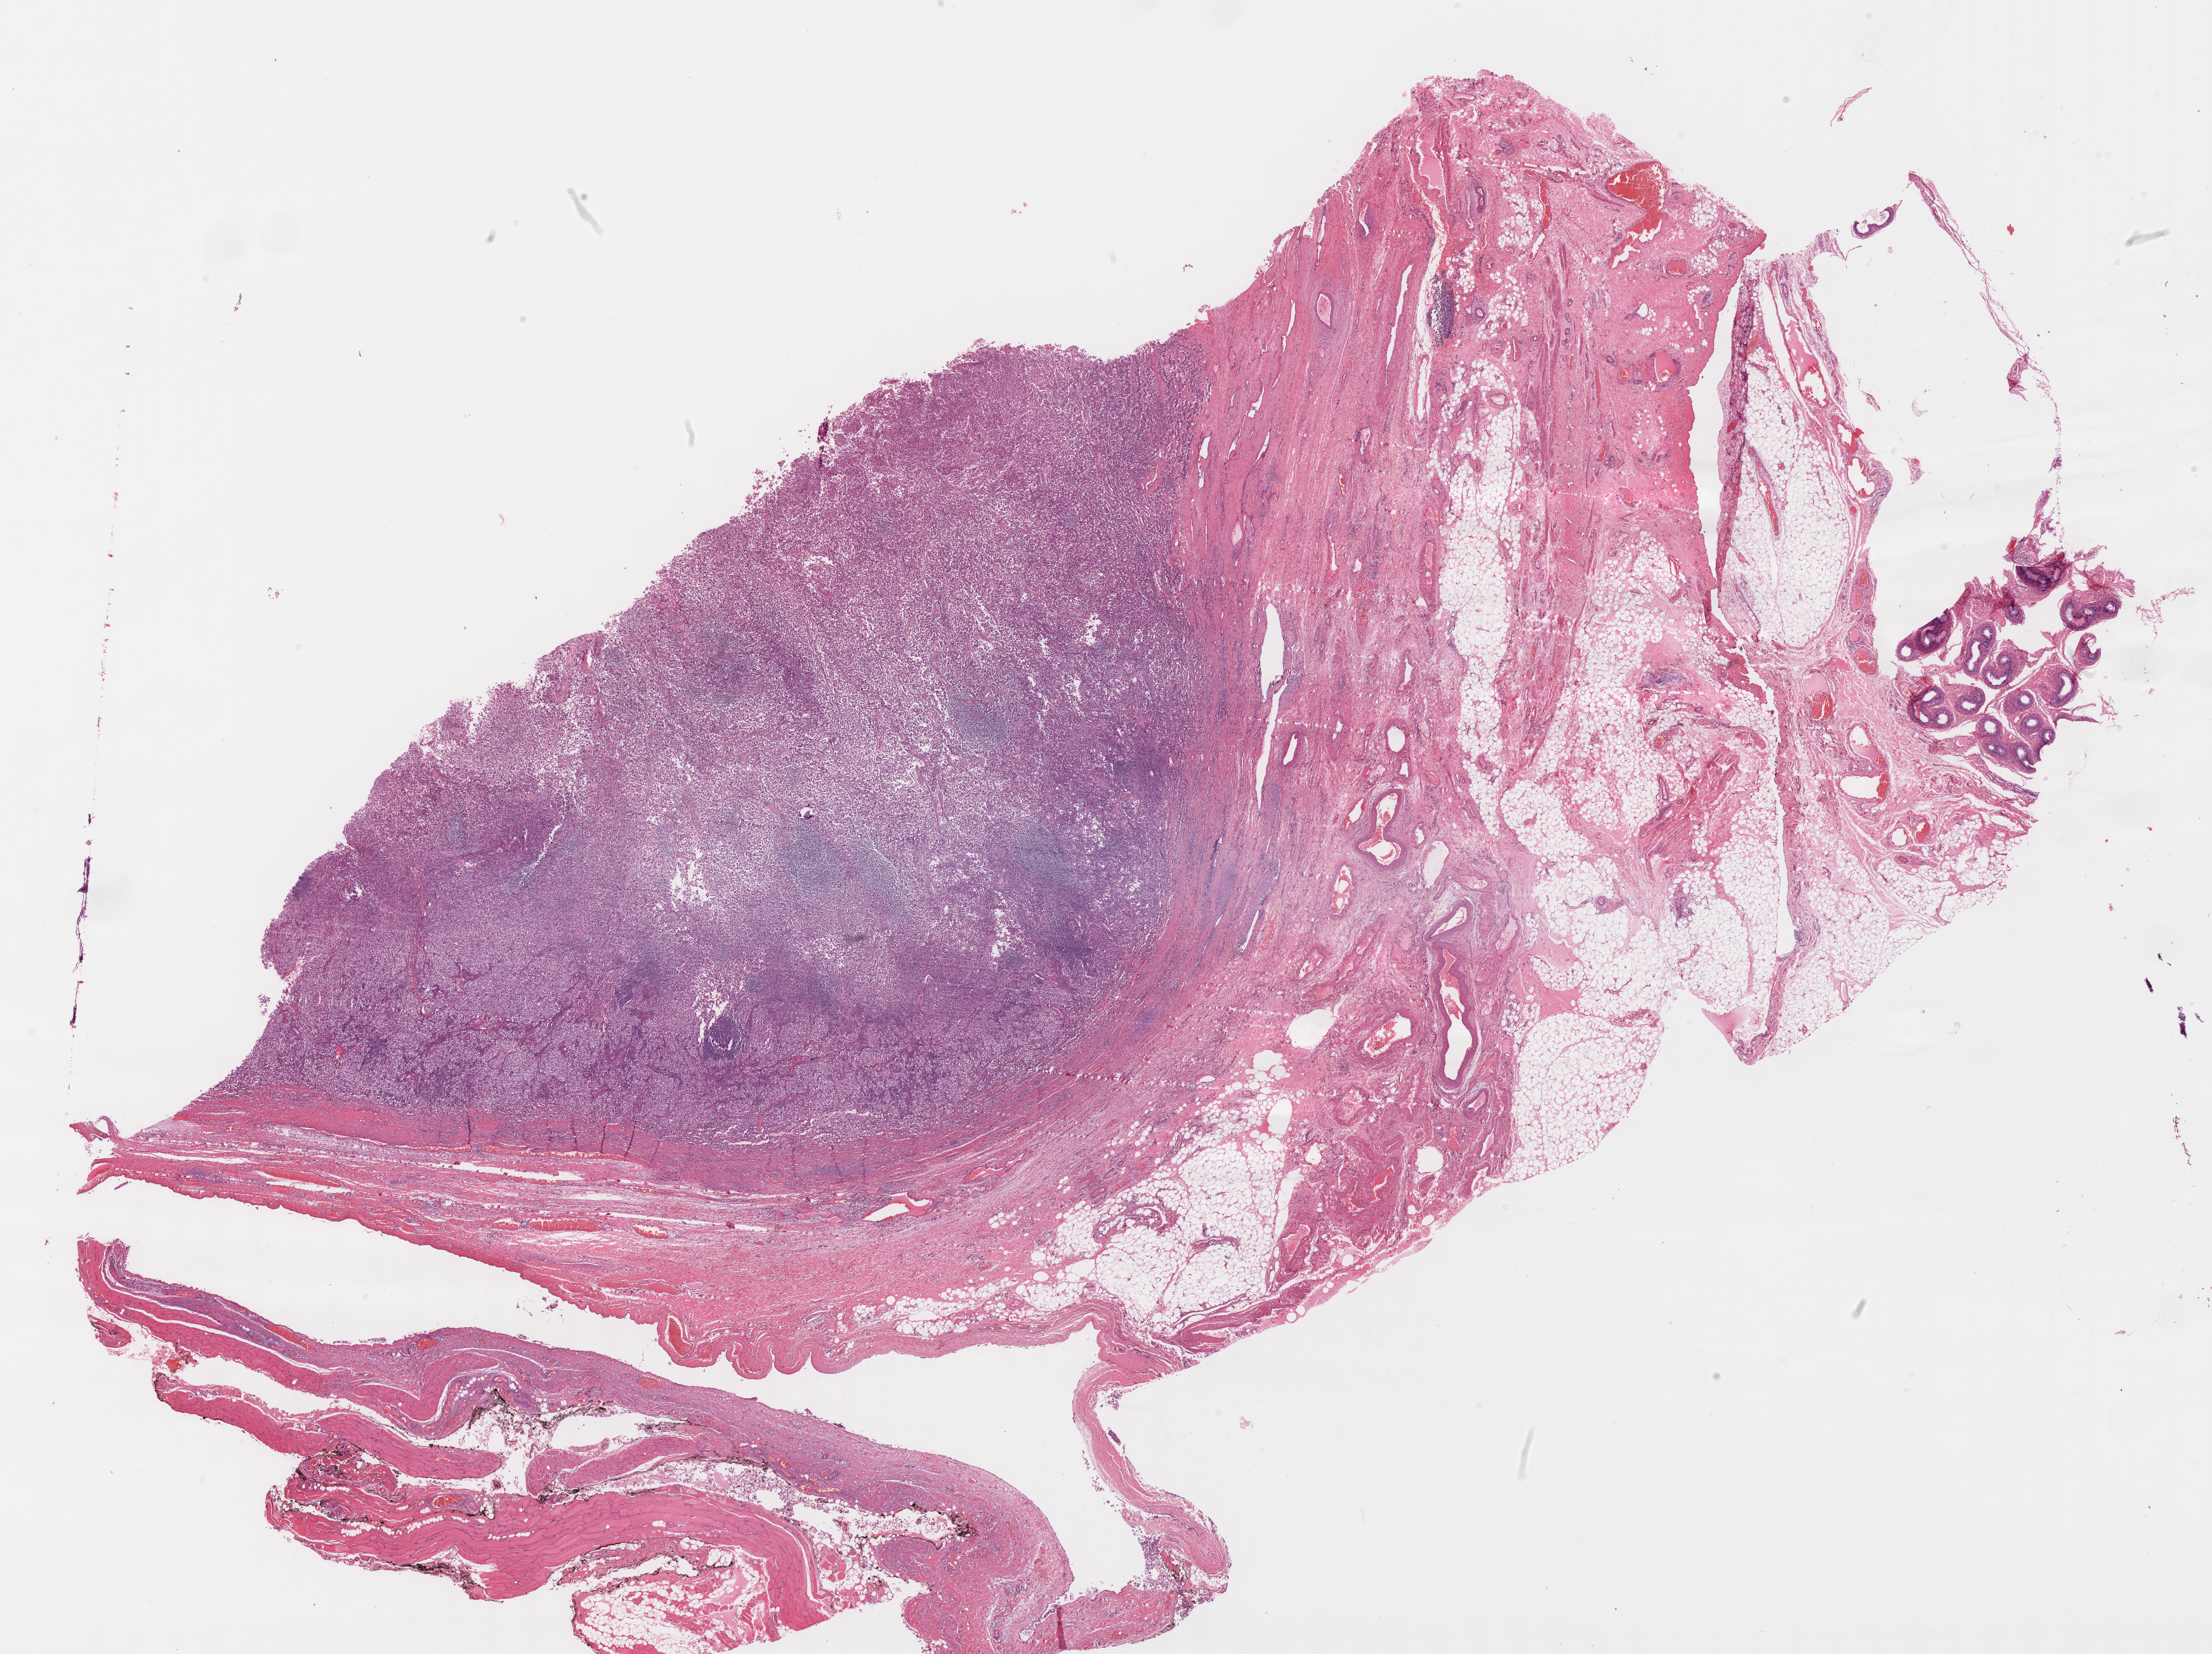
H&E-stained whole-slide image, low-resolution overview of the scanned area, about 28.2 x 21.1 mm (from a 40x scan), formalin-fixed paraffin-embedded (FFPE) diagnostic section, primary tumour sample from the testis. Male patient; age at initial diagnosis 50 years.
TNM: T1 NX M0. Diagnosis: Seminoma, NOS. AJCC pathologic stage: IA (6th edition).